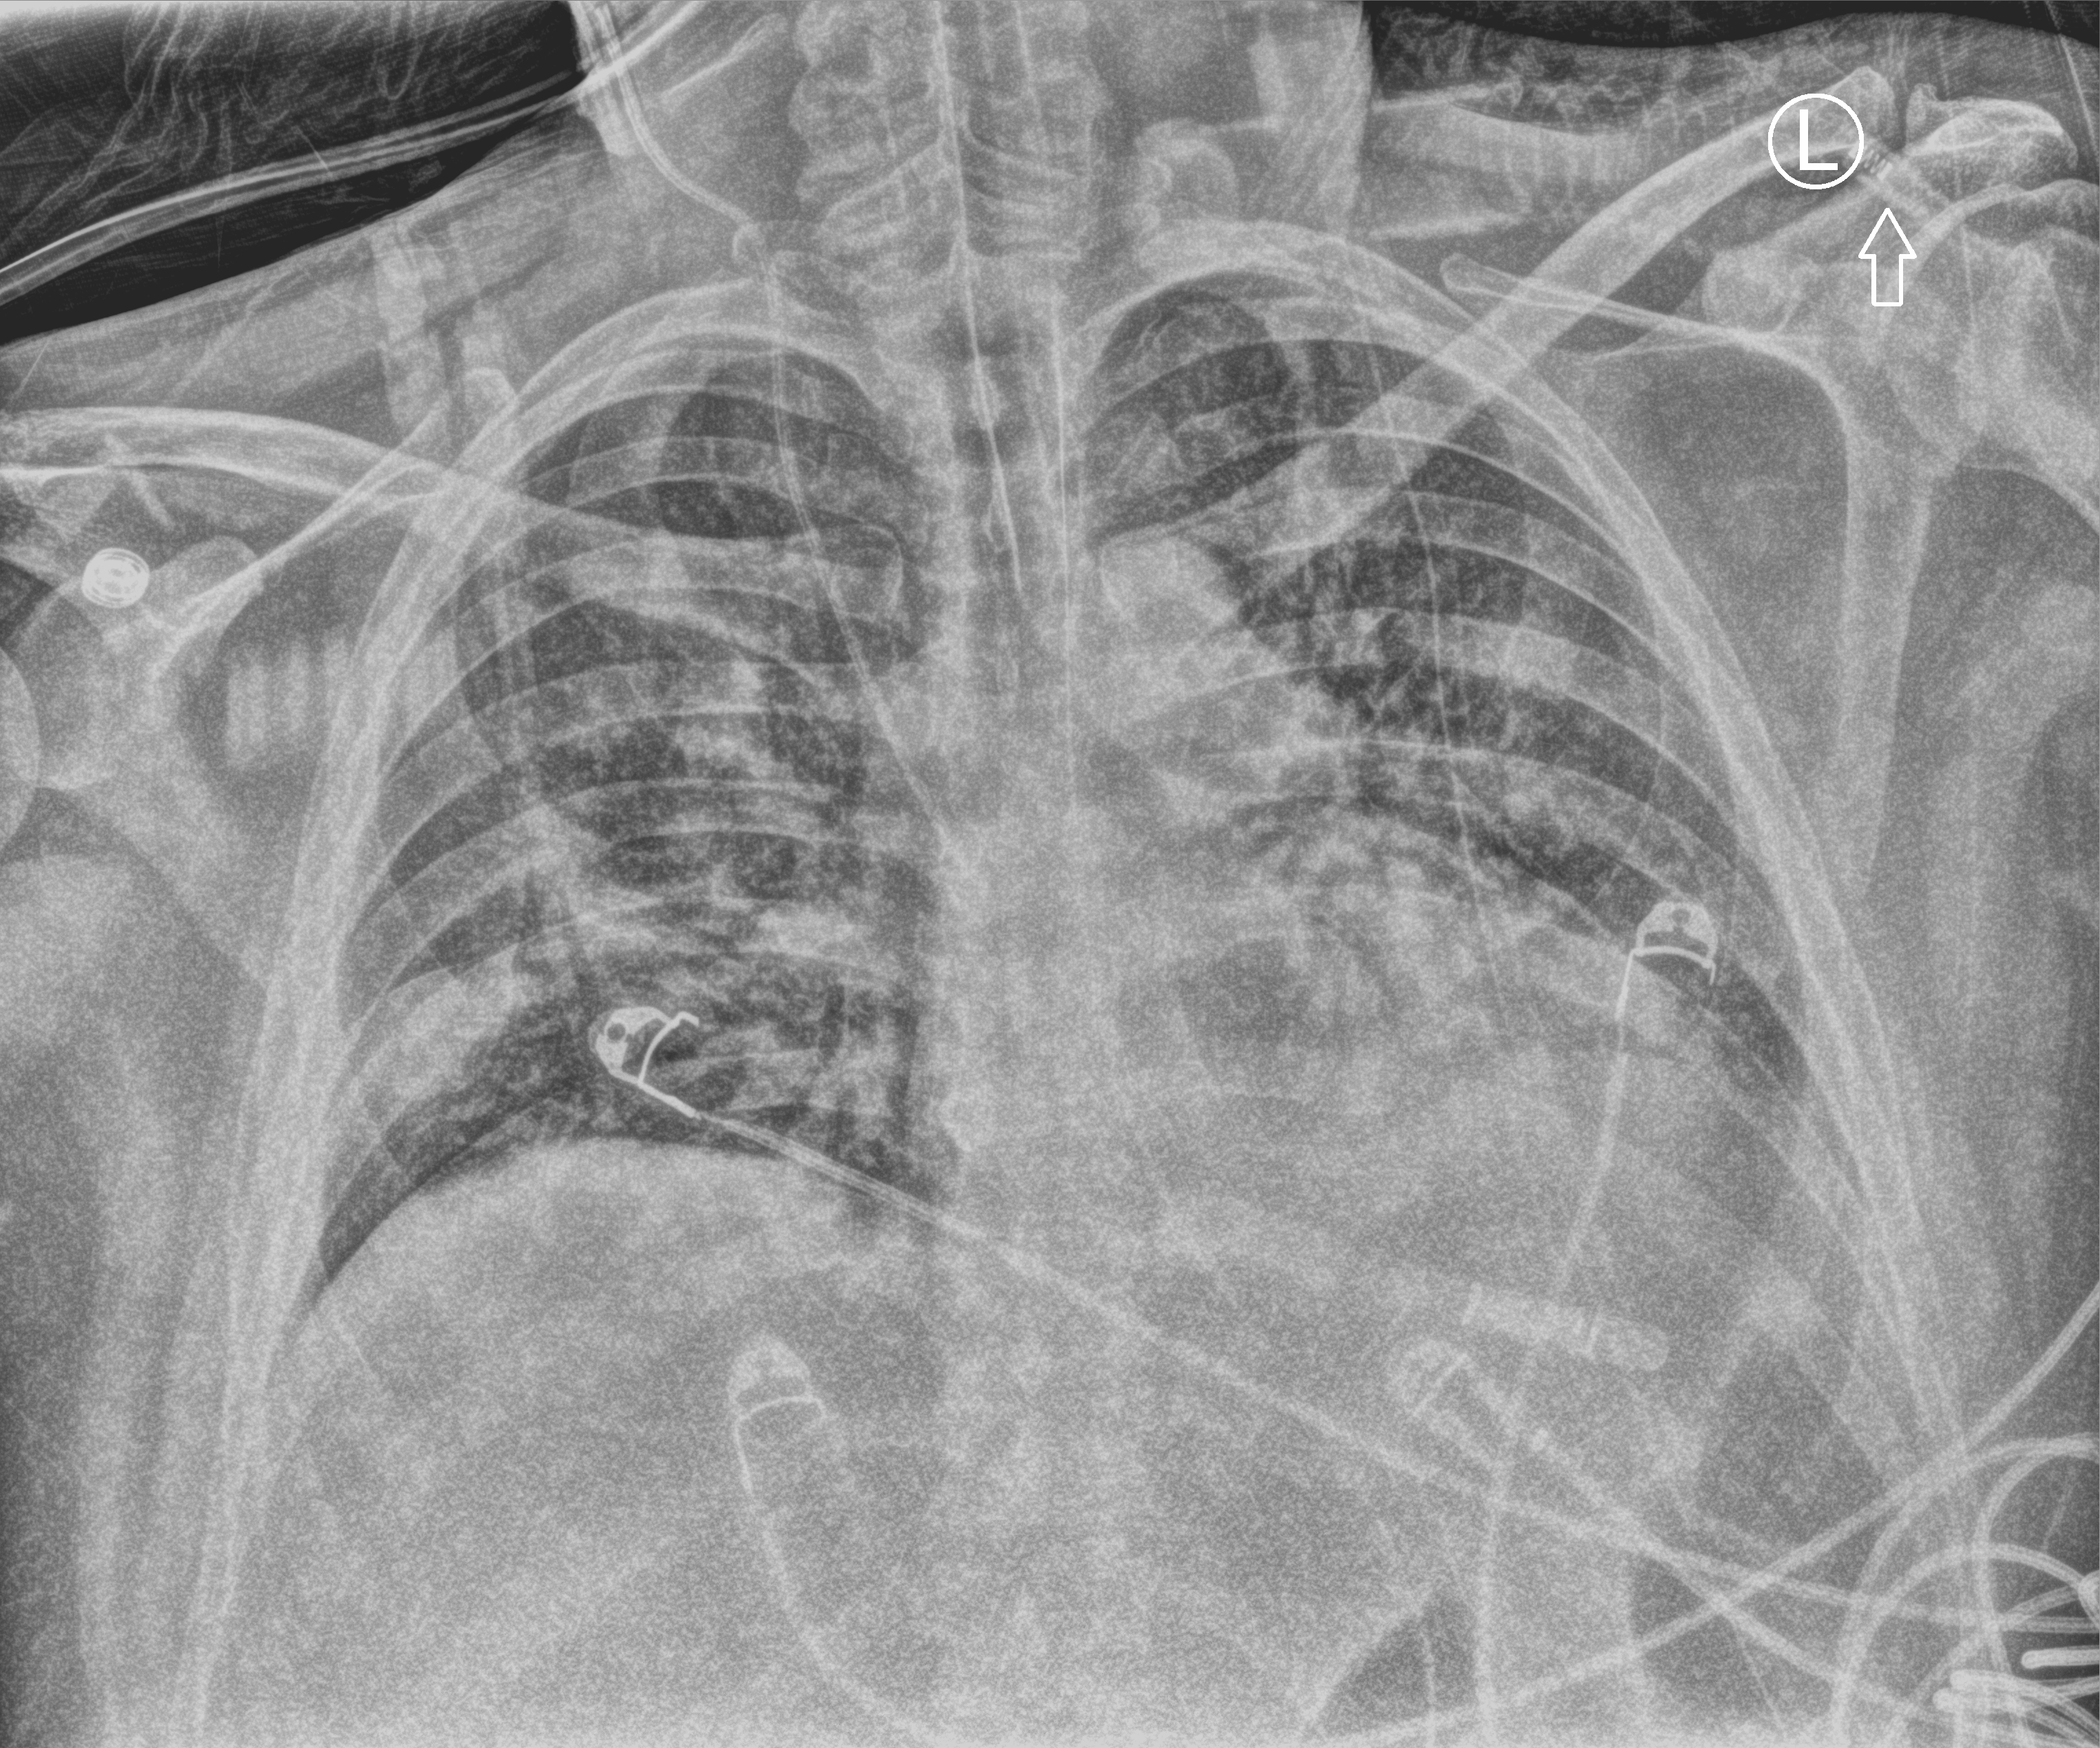
Portable chest radiograph; anteroposterior (AP) projection. Male patient hospitalised with COVID-19, age 18–59 years.
From the hospital-stay record, not from the radiograph (when in the stay this image was taken is not recorded):
- length of hospital stay: 39 days
- mechanically ventilated during this hospital stay: yes